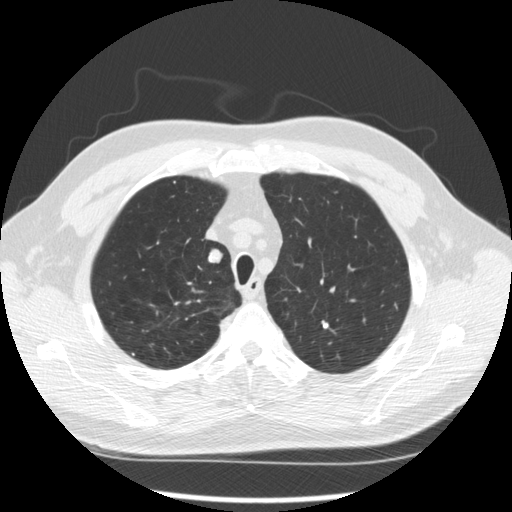
Chest CT (low-dose screening protocol), one axial image, second annual screen, lung window (W 1500 / L -600 HU), 2.5 mm slice thickness. Male, age 64 years at enrolment. Former smoker at enrolment.
Lesion marked by an expert reader, box from (x=193, y=245) to (x=226, y=274) px. The screening reader recorded 3 non-calcified nodules or masses ≥4 mm on this exam; which of them this box marks is not recorded. Official screen result: positive, other. Participant outcome: lung cancer diagnosed 411 days after this screen (after the third annual screen) — adenocarcinoma, NOS, right upper lobe, moderately differentiated (G2), stage IA (AJCC 6th edition), 14 mm at pathology.